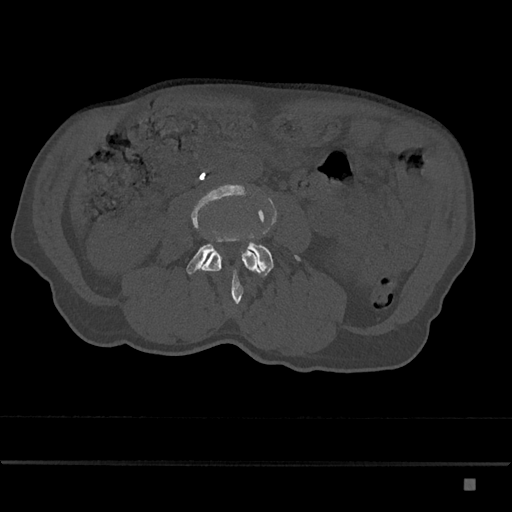
CT including the spine, one axial slice. Bone window (W 1800 / L 400 HU). 0.5 mm slice thickness. 512 × 512 image matrix, field of view 390 × 390 mm. Male patient, age 72 years. Case-level facts recorded for this patient, not image findings: primary cancer: prostate.
Outlined on this slice (semi-automatically segmented with operator editing):
- L3 vertebra: box from (x=191, y=184) to (x=260, y=304) px
- L4 vertebra: (x=186, y=241)–(x=301, y=277)